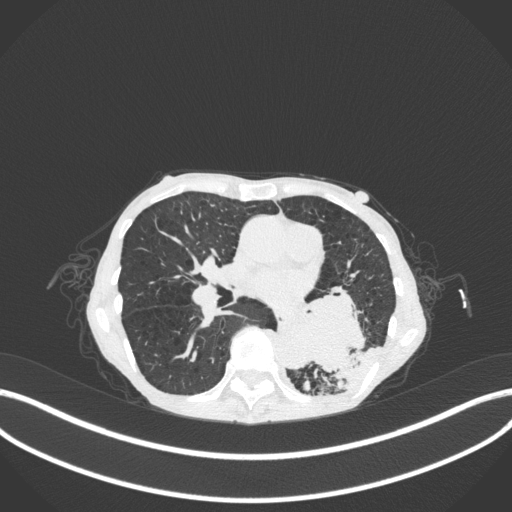
Chest CT, one axial slice. Slice 136 of 347 in the series (ordered by position). 120 kVp. Lung window (W 1500 / L -600 HU). 1 mm slice thickness. 512 × 512 image matrix, field of view 400 × 400 mm. Patient: female, 70 years. Case-level facts recorded for this patient, not image findings: clinical TNM (as recorded): T3 N0 M0; histopathological grade: G3.
Outlined on this slice (rectangle marked by the reading radiologist):
- lung tumour (recorded histology: small cell carcinoma): bounding box (x1, y1, x2, y2) in pixels: (285, 285, 372, 384)